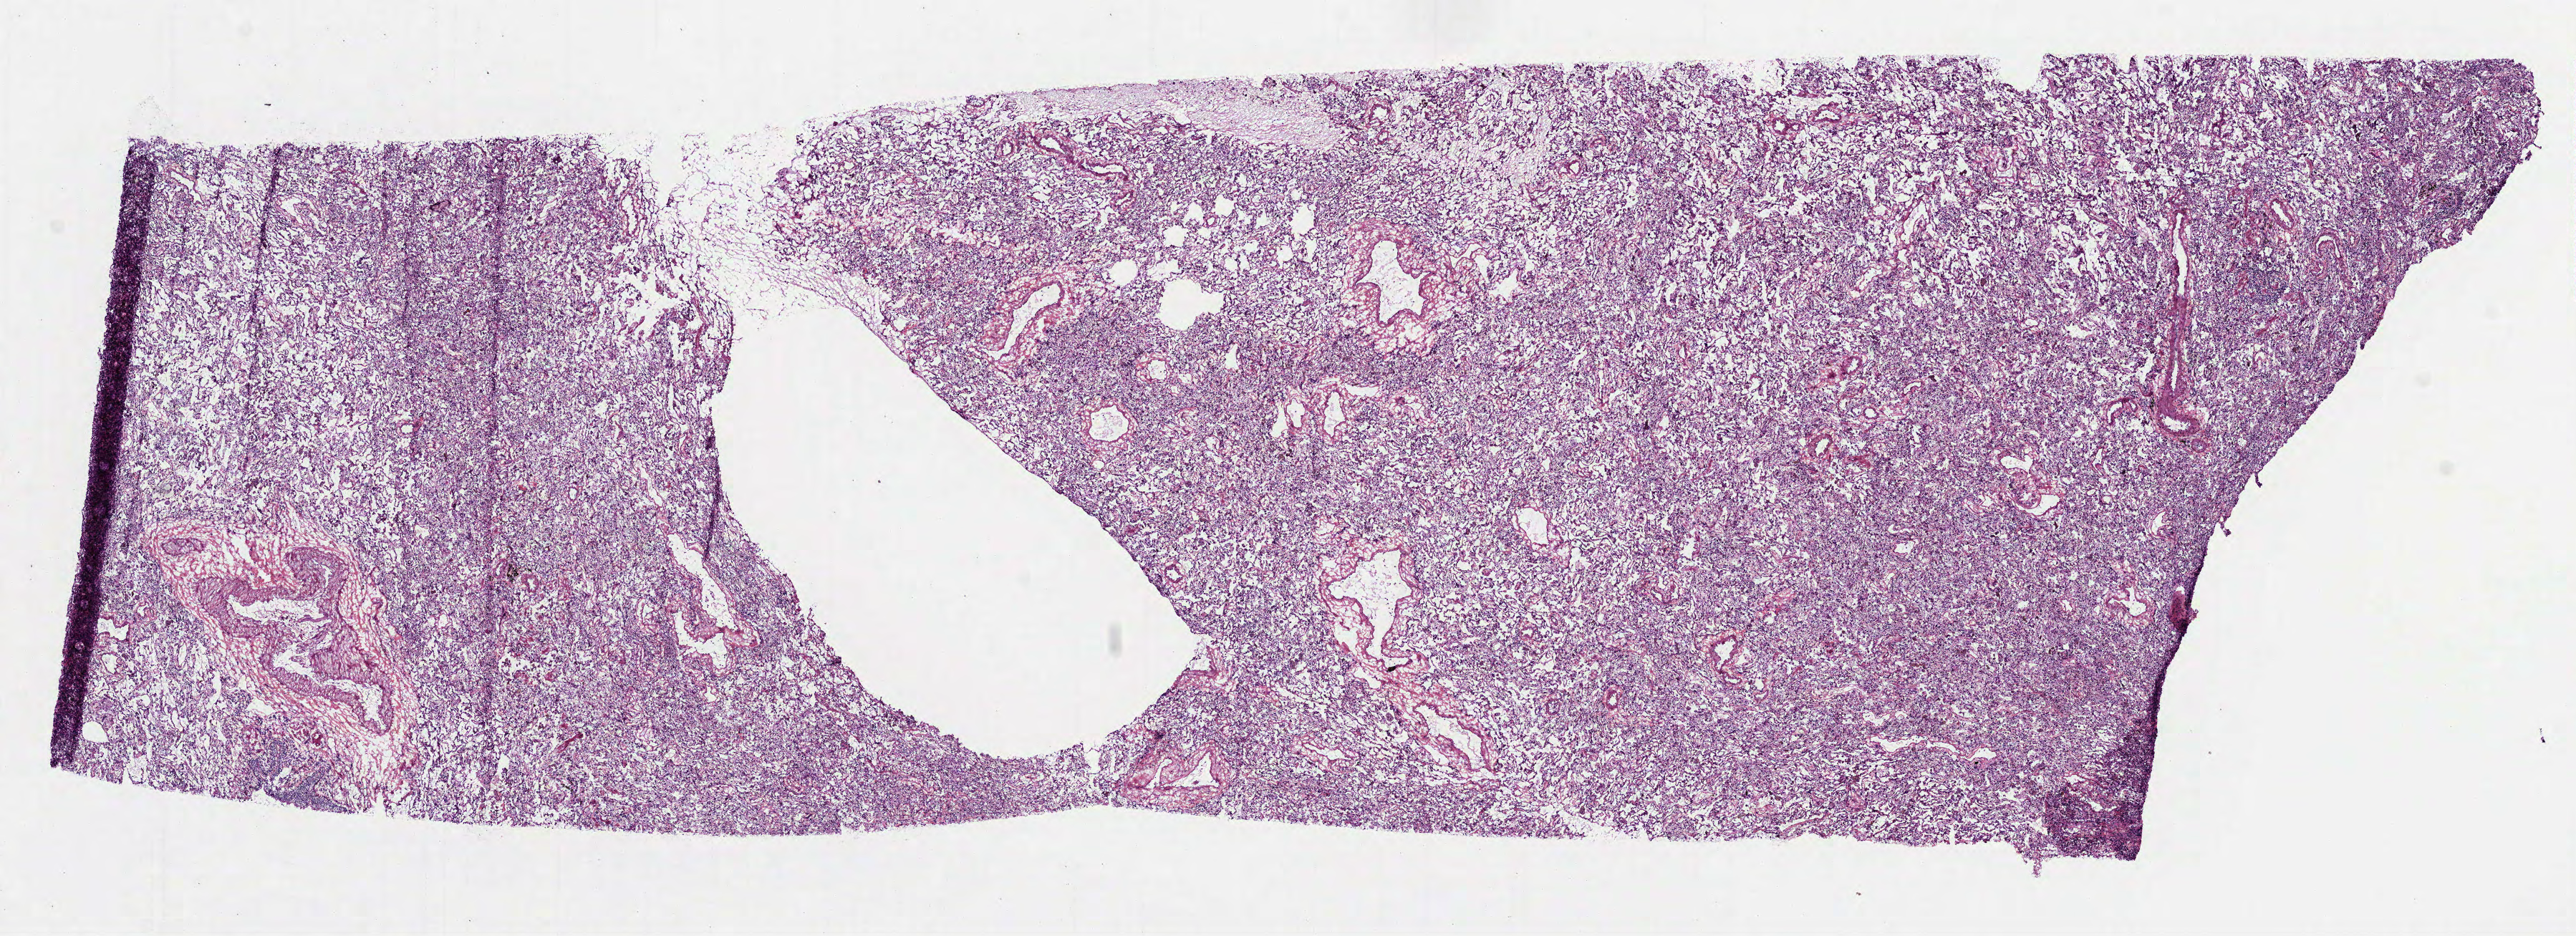
H&E whole-slide image — low-resolution overview of the scanned area, about 14.5 x 5.3 mm (from a 40x scan), frozen section from the top of the tissue portion, lung, solid tissue normal (non-tumour tissue) sample. Male patient; age at initial diagnosis 61 years.
This section: solid tissue normal sample (biorepository sample class). Patient diagnosis: Squamous cell carcinoma, NOS (upper lobe, lung).